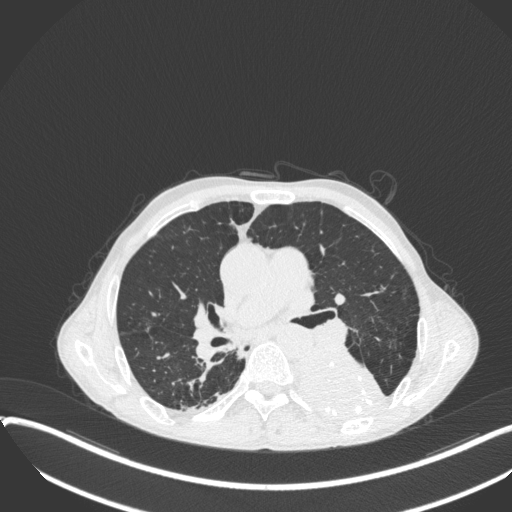
Chest CT, one axial slice. Slice 214 of 400 in the series (ordered by position). Reconstruction kernel B31f. 120 kVp. Lung window (W 1500 / L -600 HU). 1 mm slice thickness. 512 × 512 image matrix, field of view 400 × 400 mm. Male patient, age 57 years. Case-level facts recorded for this patient, not image findings: clinical TNM (as recorded): T4 N0 M0.
Structures marked on this image (bounding box drawn by a radiologist):
- lung tumour (recorded histology: squamous cell carcinoma): box from (x=275, y=338) to (x=383, y=425) px